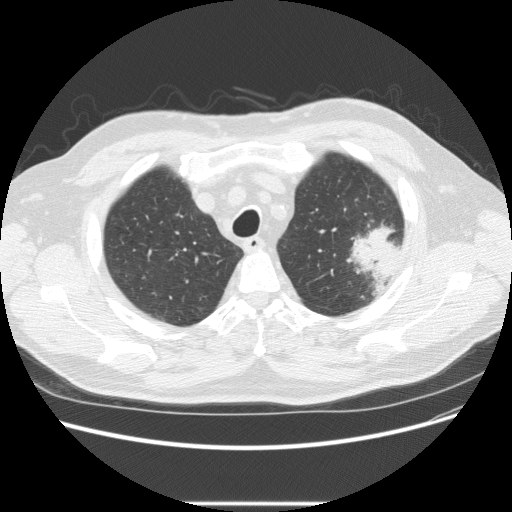
Low-dose screening chest CT, one axial slice. Reconstruction kernel STANDARD. 120 kVp. Lung window (W 1500 / L -600 HU). 2.5 mm slice thickness. 512 × 512 image matrix, field of view 380 × 380 mm.
Structures marked on this image (manually delineated by an expert):
- lesion 1 (tumor, upper lobe of left lung): bounding box <346,223,401,287> (left, top, right, bottom; pixels)